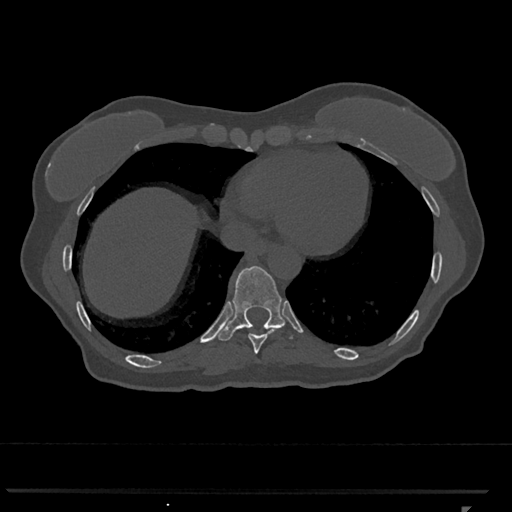
CT including the spine, one axial slice. Reconstruction kernel Br40s/3. Bone window (W 1800 / L 400 HU). 512 × 512 image matrix, field of view 380 × 380 mm. Patient: female, 62 years. From the clinical record (not read from this slice): primary cancer: renal.
Outlined on this slice (semi-automatic segmentation, software-assisted and operator-edited):
- T10 vertebra: box from (x=218, y=266) to (x=293, y=341) px
- T9 vertebra: (x=248, y=326)–(x=291, y=354)